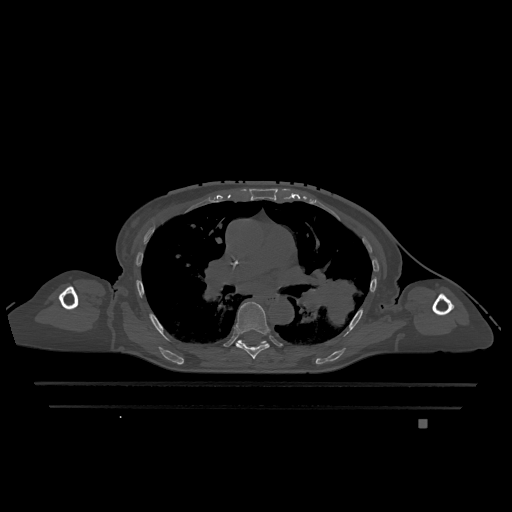
CT including the spine, one axial slice; bone window (W 1800 / L 400 HU); 0.5 mm slice thickness; 512 × 512 image matrix, field of view 500 × 500 mm. Female patient, age 74 years. Case-level facts recorded for this patient, not image findings: primary cancer: lung; vertebrae with lytic lesions (as recorded): T1, T4, T5, T6, L4, L5.
Annotated regions visible in this slice (semi-automatically segmented with operator editing):
- T6 vertebra: bounding box <235,302,270,359> (left, top, right, bottom; pixels)
- T7 vertebra: <237,340,268,344>